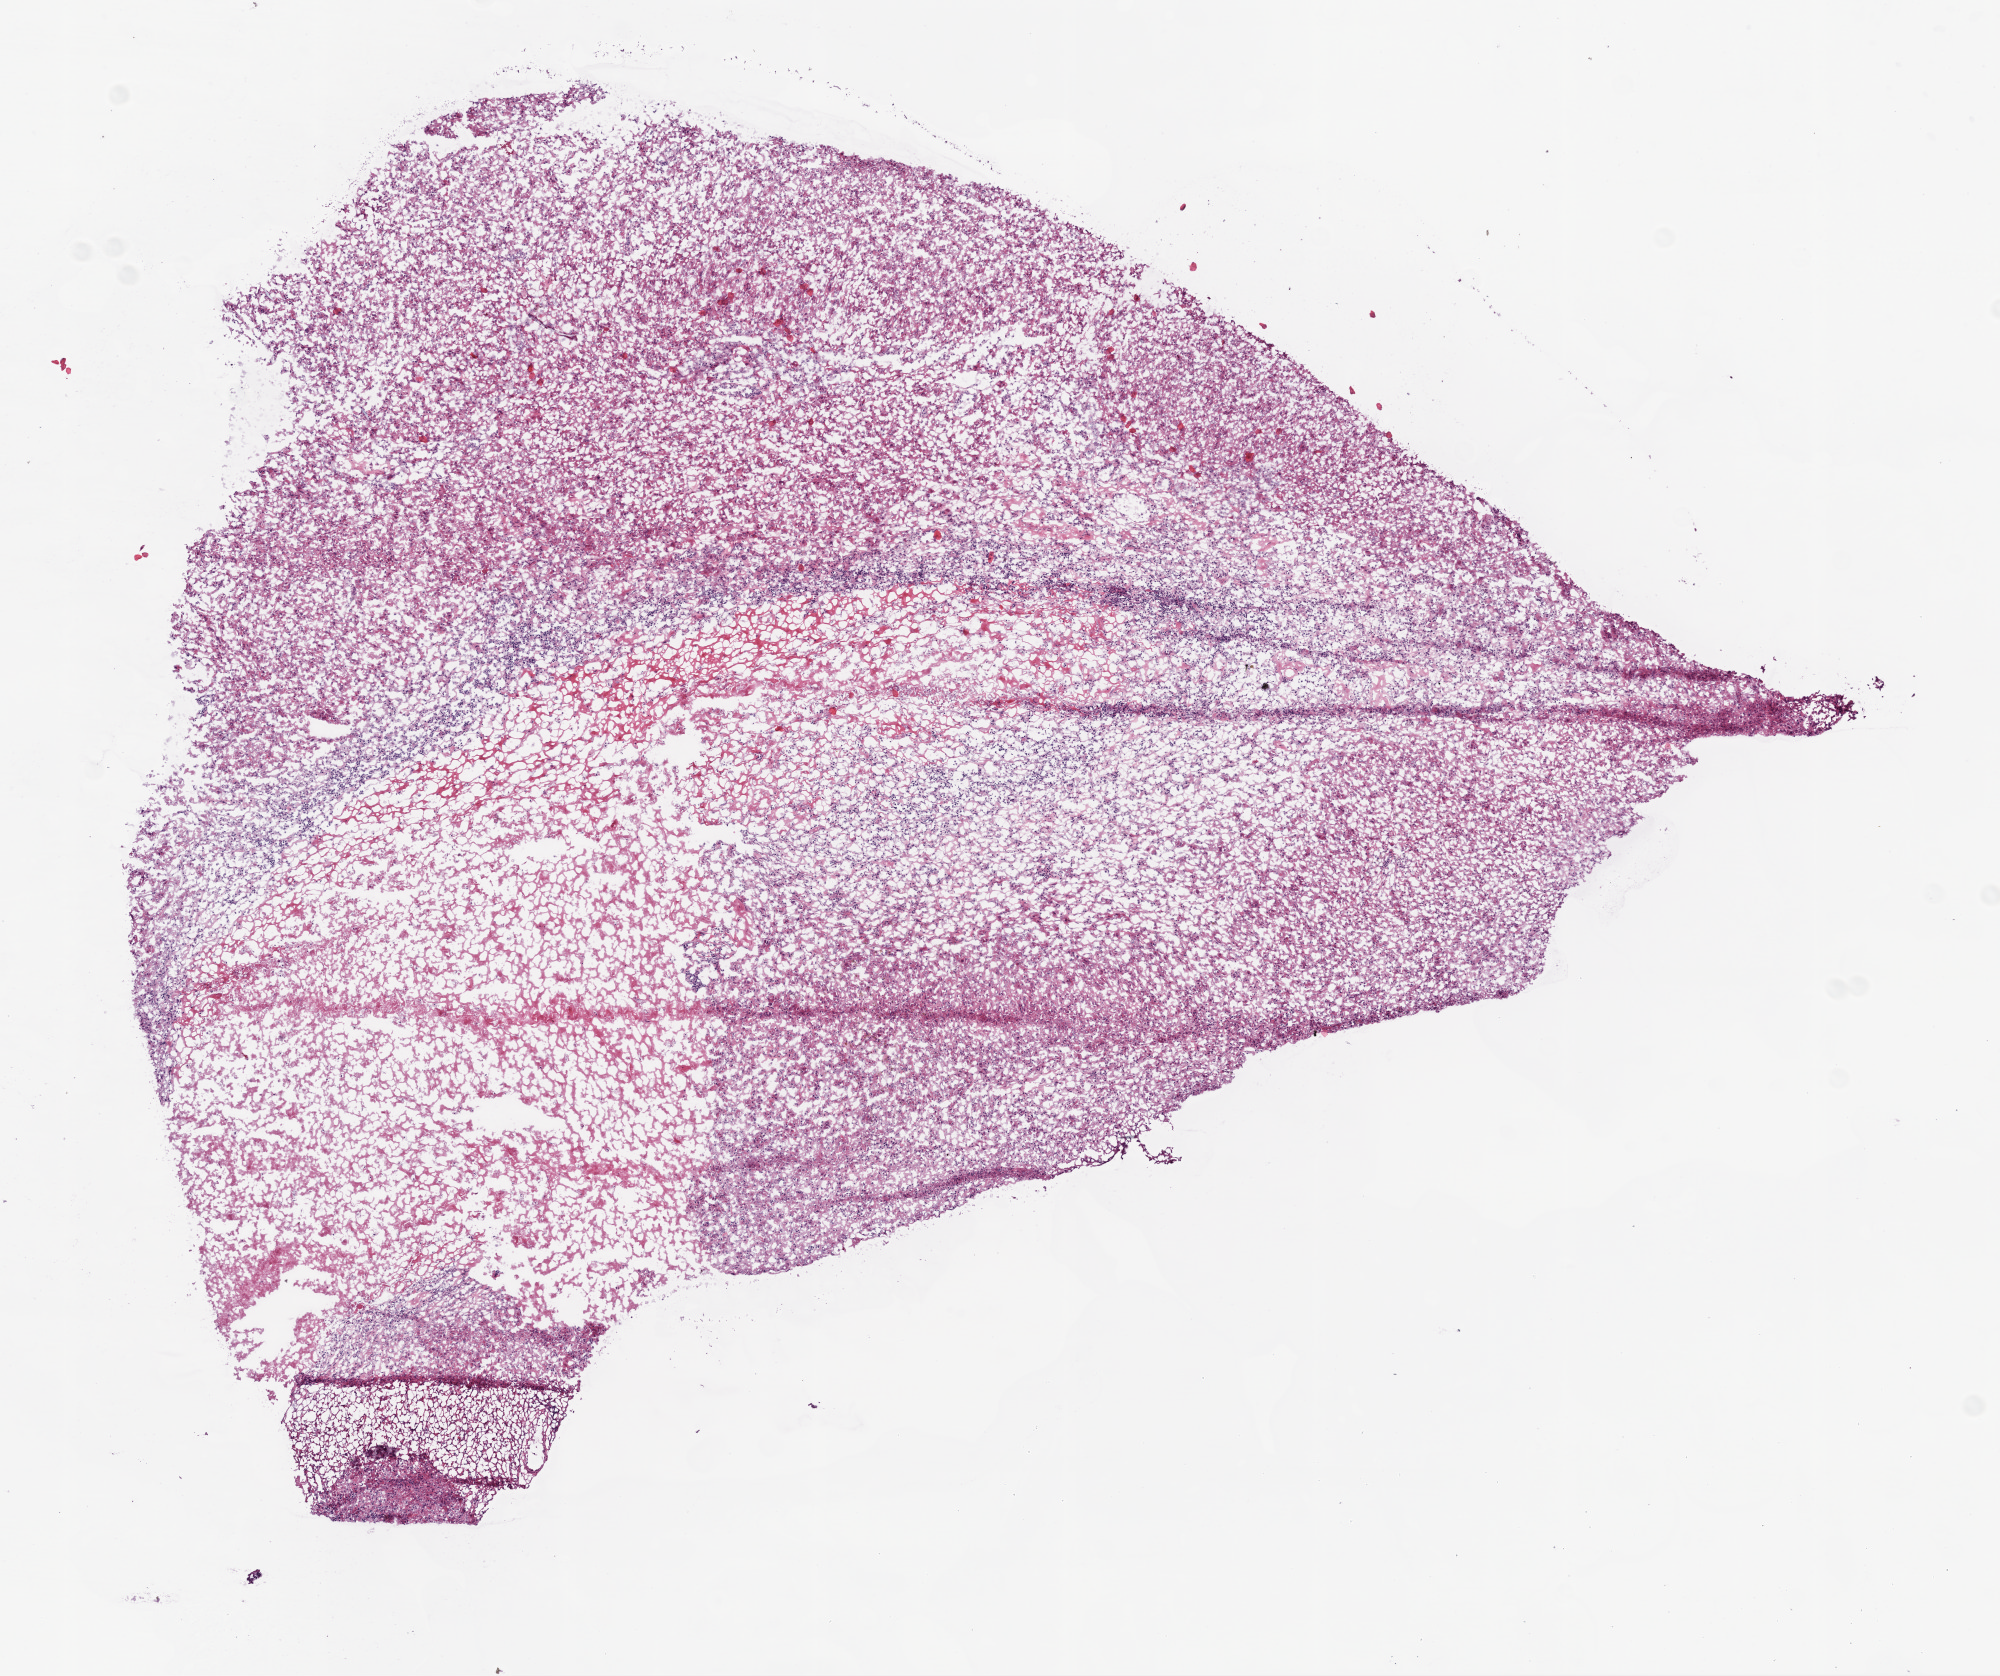
Whole-slide histology image, Hematoxylin and eosin (H&E) stained — a low-resolution overview of the entire scanned area, about 8.0 x 6.7 mm (slide scanned at 20x), frozen section from the bottom of the tissue portion, primary tumour sample from the brain. Male, age 76 years at initial diagnosis. Composition of this section per pathologist review: tumour cells 70%, tumour nuclei 90%, normal cells 0%, stromal cells 5%, necrosis 25%.
Pathologic diagnosis: Glioblastoma.